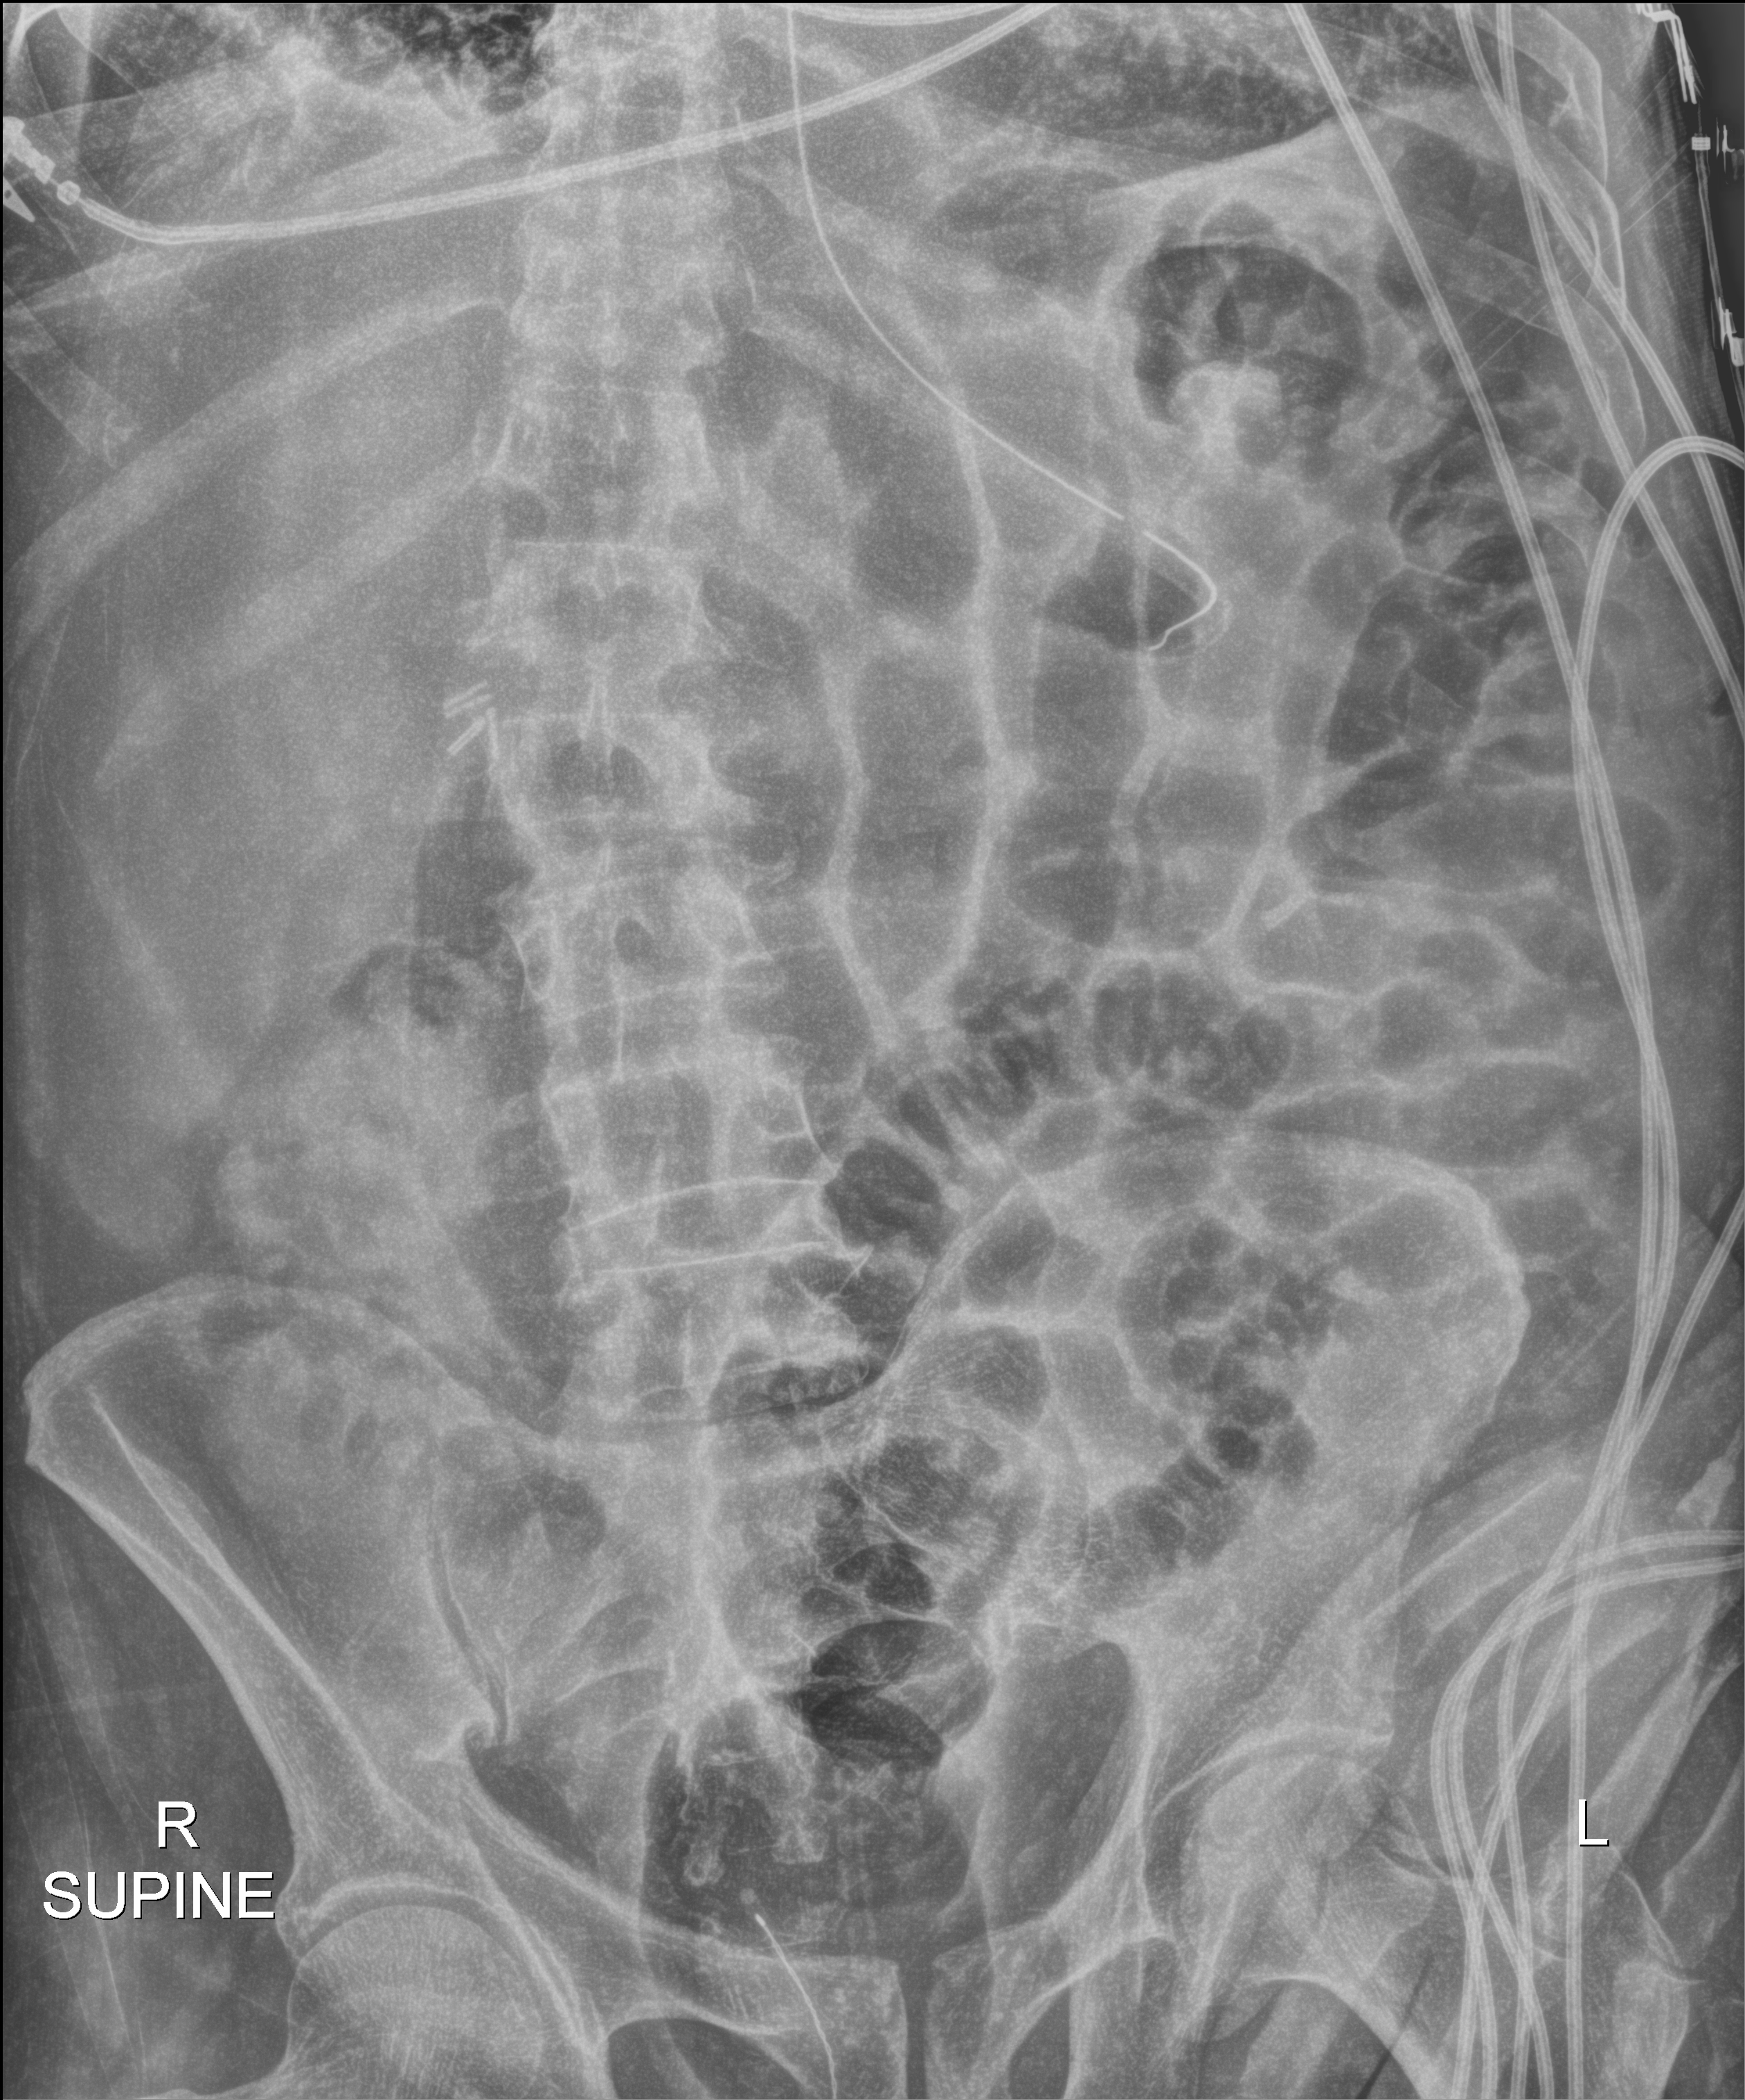
Abdomen X-ray (portable); anteroposterior (AP) projection. Patient hospitalised with COVID-19; male, aged 75–90 years.
Hospital-stay facts (about this admission, not read from this image; timing relative to this image not recorded):
- mechanically ventilated during this hospital stay: yes